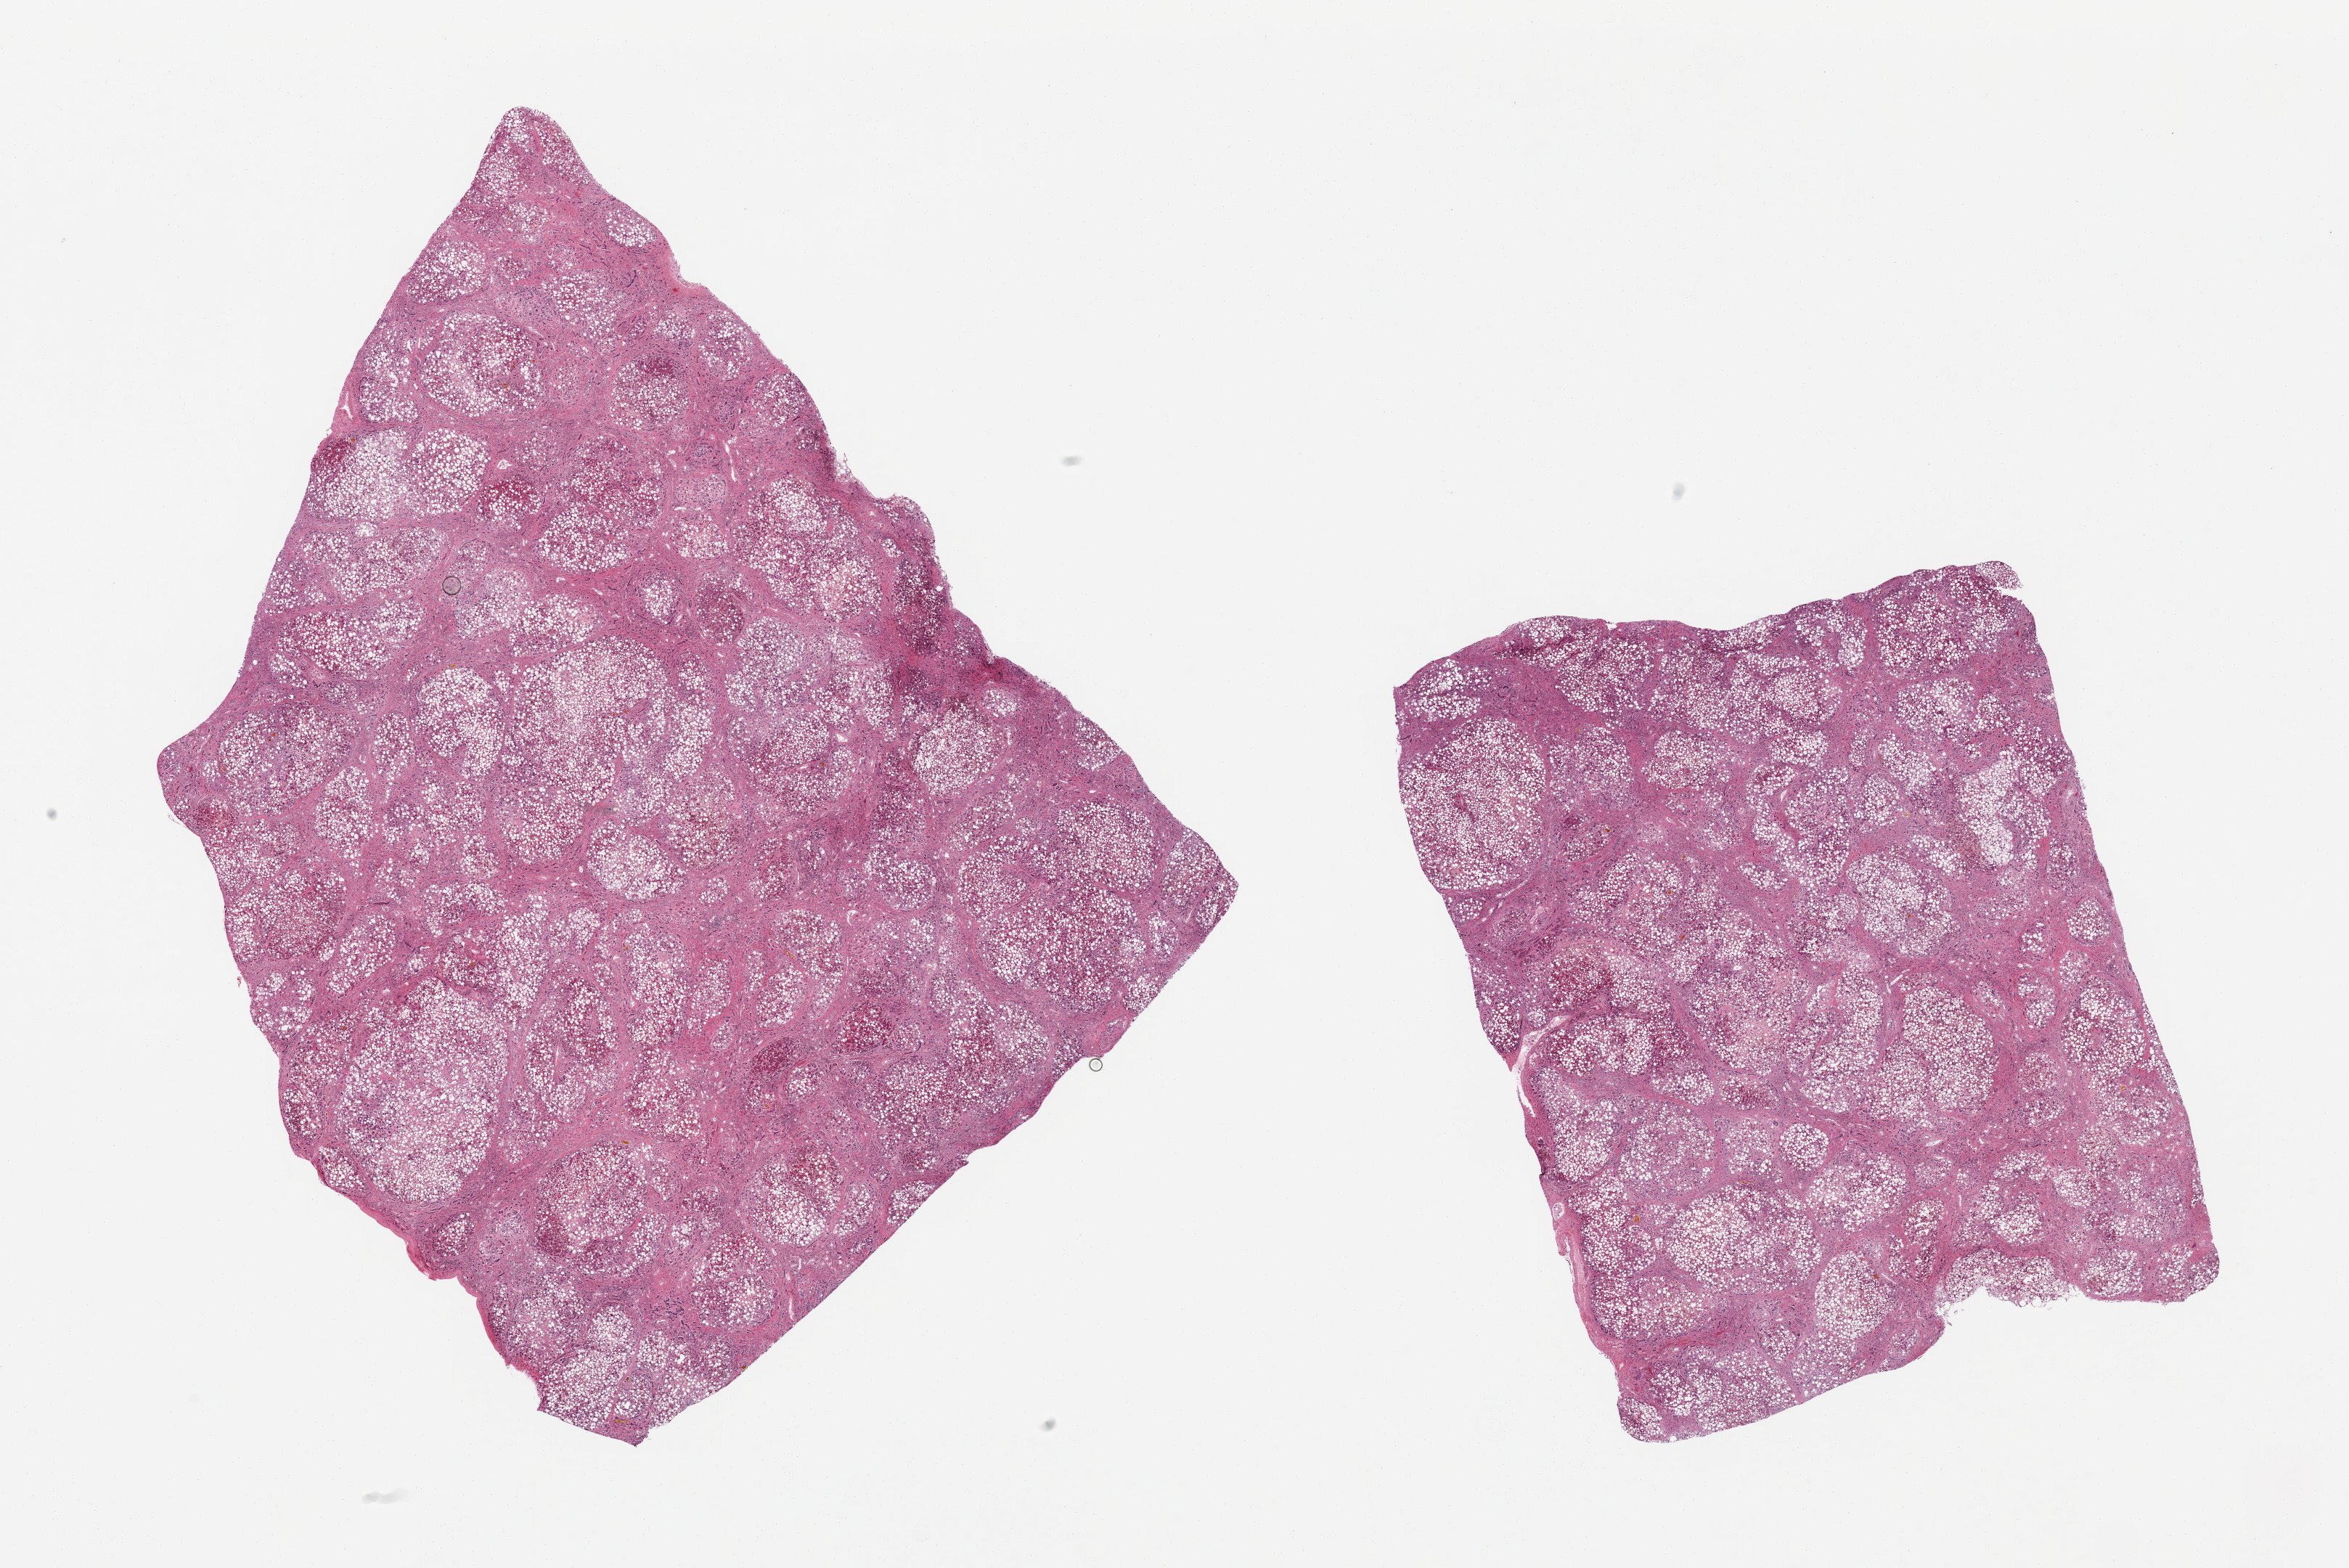
Digitized H&E-stained section, whole scanned area (about 25.6 x 17.1 mm) shown as a low-resolution overview; PAXgene-fixed, paraffin-embedded tissue; section of liver (target tissue); tissue donor sample. Donor sex: male.
* review note (as recorded): 2 pieces, established cirrhosis, diffuse steatohepatitis, mixed pattern